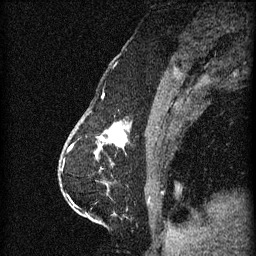
Breast MRI (dynamic contrast-enhanced), one sagittal slice. Position 22 of 60 along the scan axis. 3 images stored at this slice position (order not interpretable as contrast timing). 1.5 T. TE 4.2 ms, TR 11 ms. 1.5 mm slice thickness. 256 × 256 image matrix, field of view 180 × 180 mm. Female patient, age 63 years.
Outlined on this slice (semi-automatically segmented with operator editing):
- analysis volume of interest (the breast-tissue region the enhancement analysis was run in; not a lesion): box from (x=94, y=120) to (x=133, y=153) px
- tumour enhancement mask (voxels above the 70 % enhancement threshold inside the analysis volume of interest): (x=98, y=126)–(x=127, y=151)